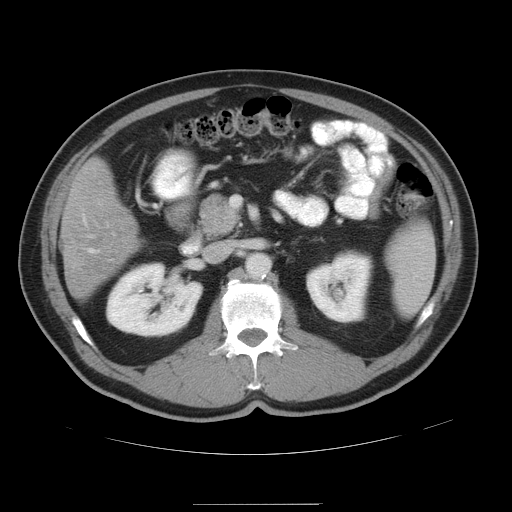
Contrast-enhanced abdominal CT, one axial slice; slice 22 of 47 in the series (ordered by position); 120 kVp; intravenous contrast given; soft-tissue window (W 400 / L 40 HU); 5 mm slice thickness; 512 × 512 image matrix, field of view 420 × 420 mm. Male patient, age 61 years. Case-level facts recorded for this patient, not image findings: diagnosis: colorectal cancer liver metastases, imaged before liver resection; multiple liver metastases: no; largest metastasis: 1.2 cm.
Outlined on this slice (manually delineated by an expert):
- hepatic veins: bounding box [x1, y1, x2, y2] px = [90, 248, 96, 252]
- liver: [63, 161, 137, 299]
- planned liver remnant (the part of the liver to remain after resection): [67, 161, 137, 264]
- liver metastasis: [61, 240, 81, 254]